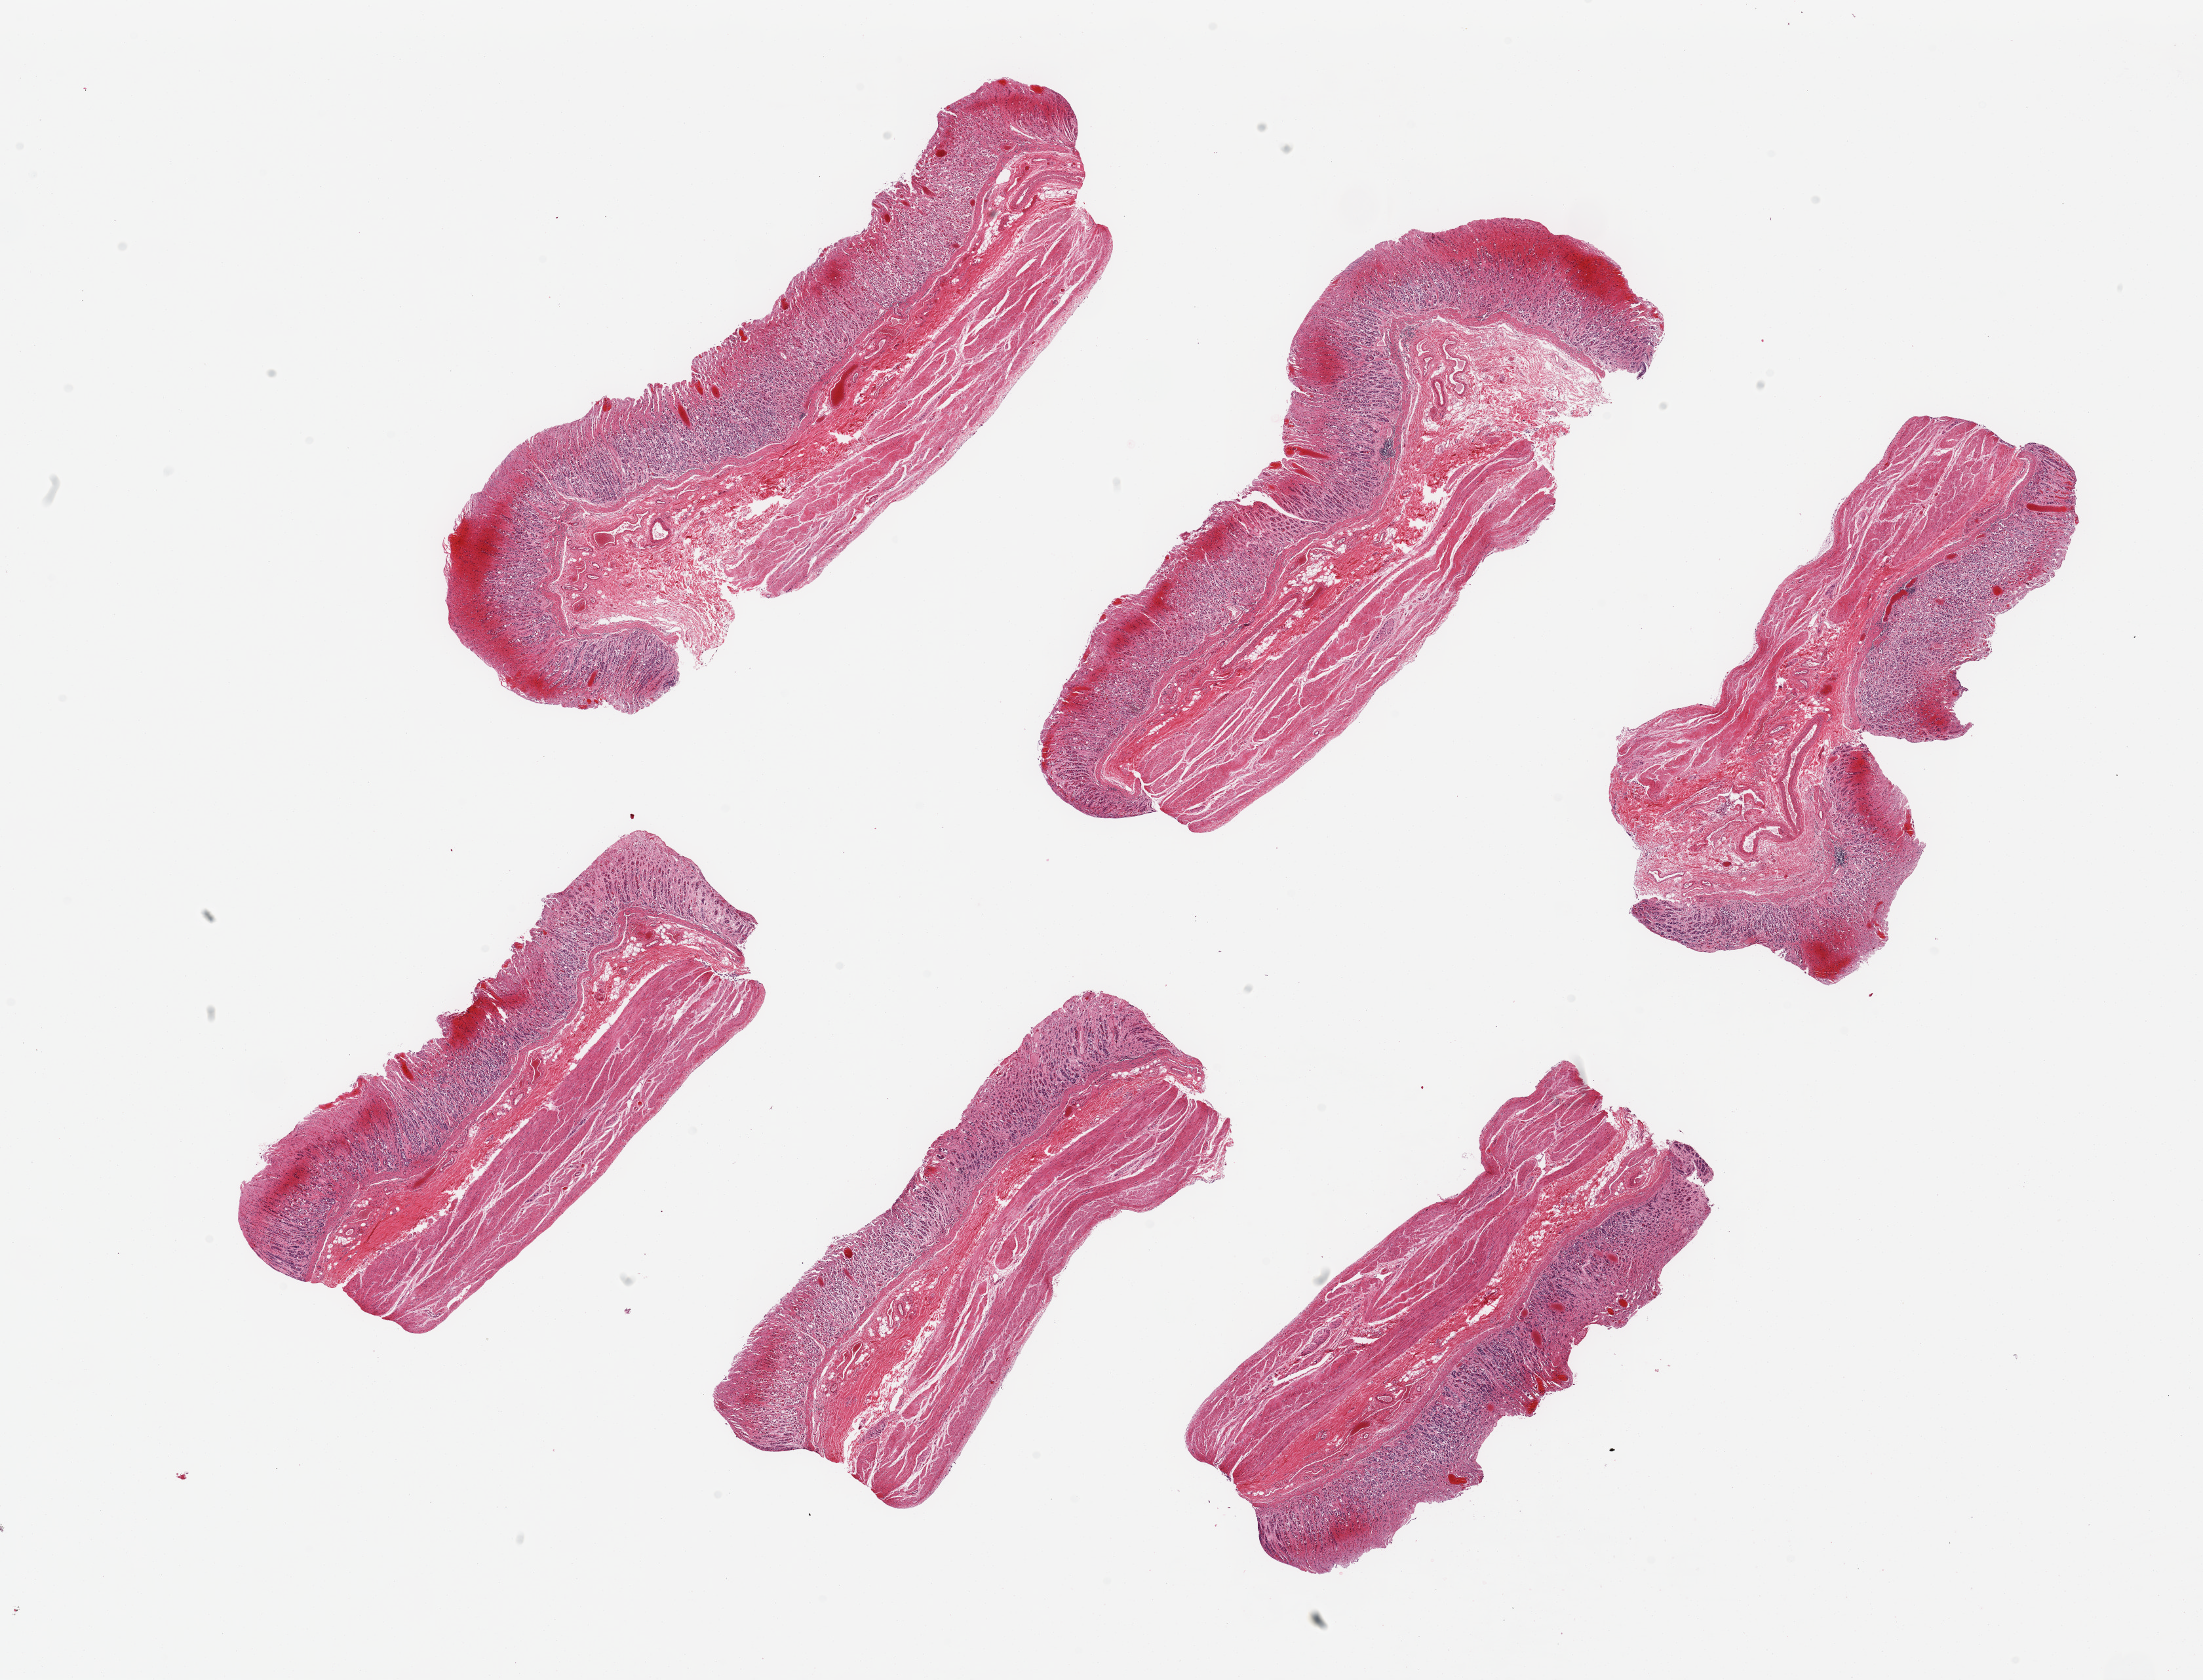
H&E whole-slide image, brightfield, shown as a low-resolution overview of the whole scanned area (about 26.6 x 20.3 mm, slide scanned at 20x), PAXgene-fixed, paraffin-embedded tissue, target tissue: stomach, tissue donor sample. Donor: male.
Pathologist's review note for this sample: 6 pieces up to 9.6x3.7 mm; severe mucosal hyperemia and superficial hemorrhages.